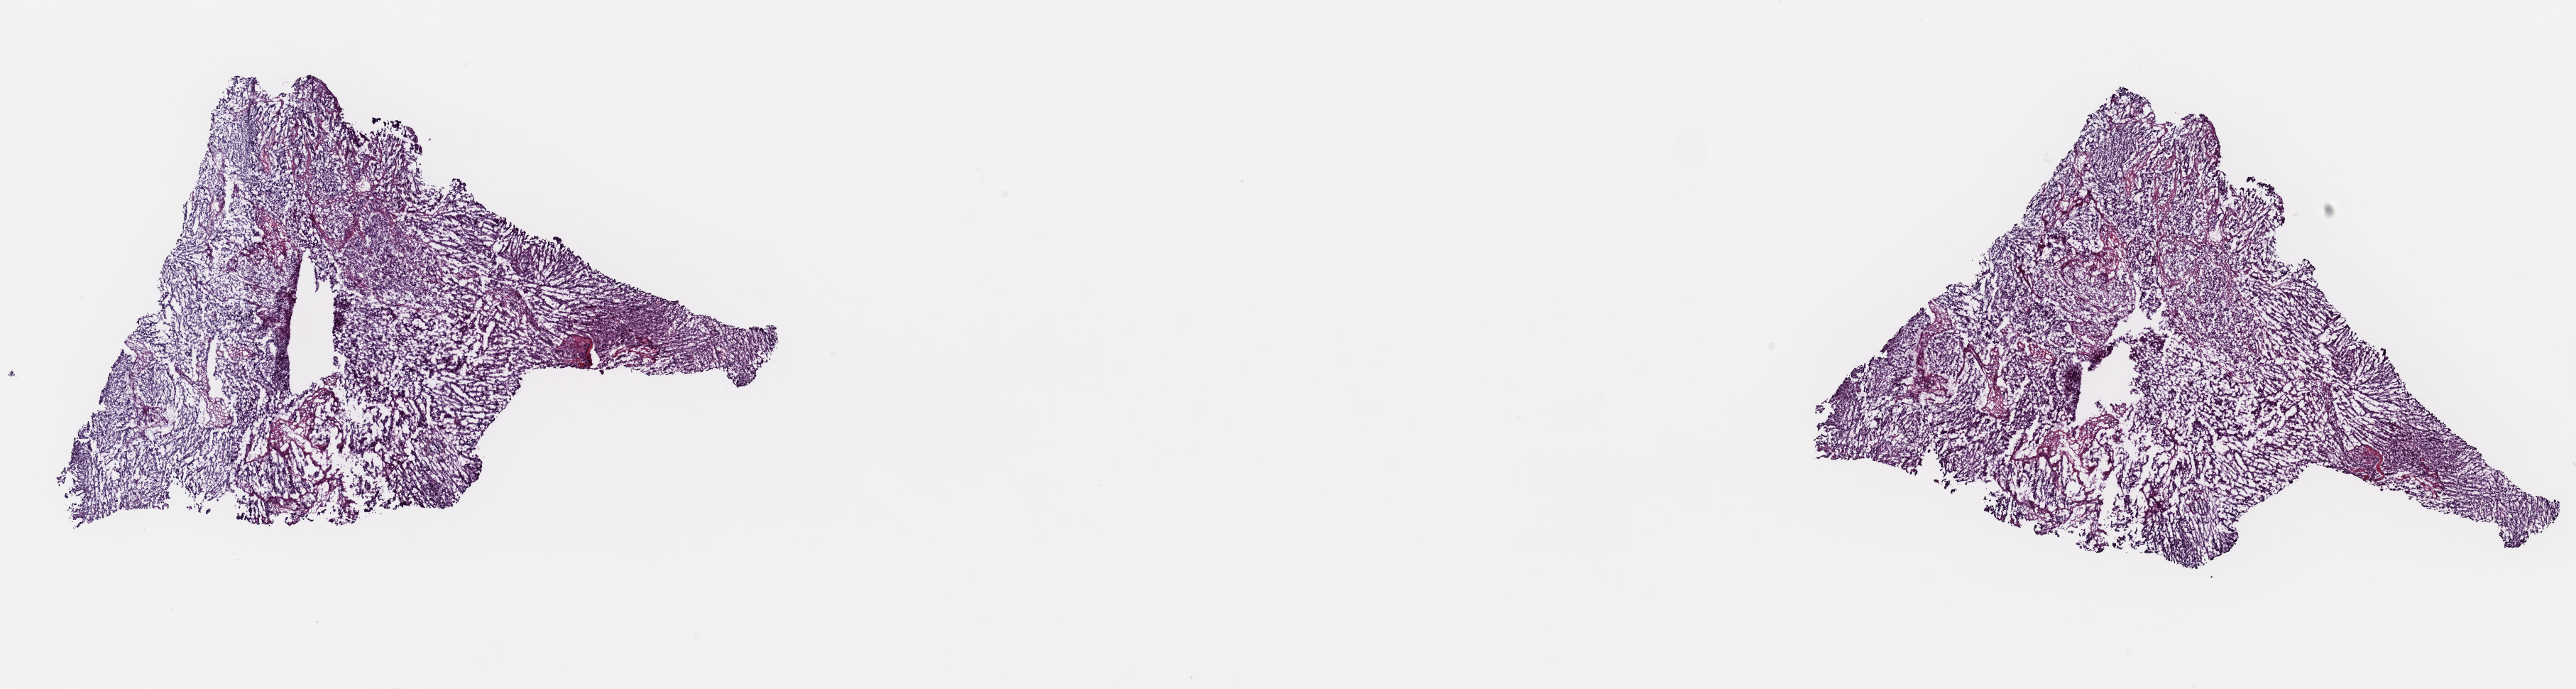
Whole-slide histology image, Hematoxylin and eosin (H&E) stained, low-resolution overview of the scanned area, about 28.7 x 7.7 mm. Frozen section from the top of the tissue portion. Primary tumour sample from the uterus. Patient: female, age at initial diagnosis 35 years. Histologic grade: G3 (poorly differentiated). Pathologist review of this section (percent, as recorded): tumour cells 70%, tumour nuclei 90%, normal cells 0%, stromal cells 25%, necrosis 5%. Inflammatory infiltration, as recorded: lymphocyte infiltration 1%, monocyte infiltration 0%, neutrophil infiltration 0%.
• lymph nodes positive (case pathology): 0 of 7 examined
• FIGO stage: IC
• histologic diagnosis: Endometrioid adenocarcinoma, NOS